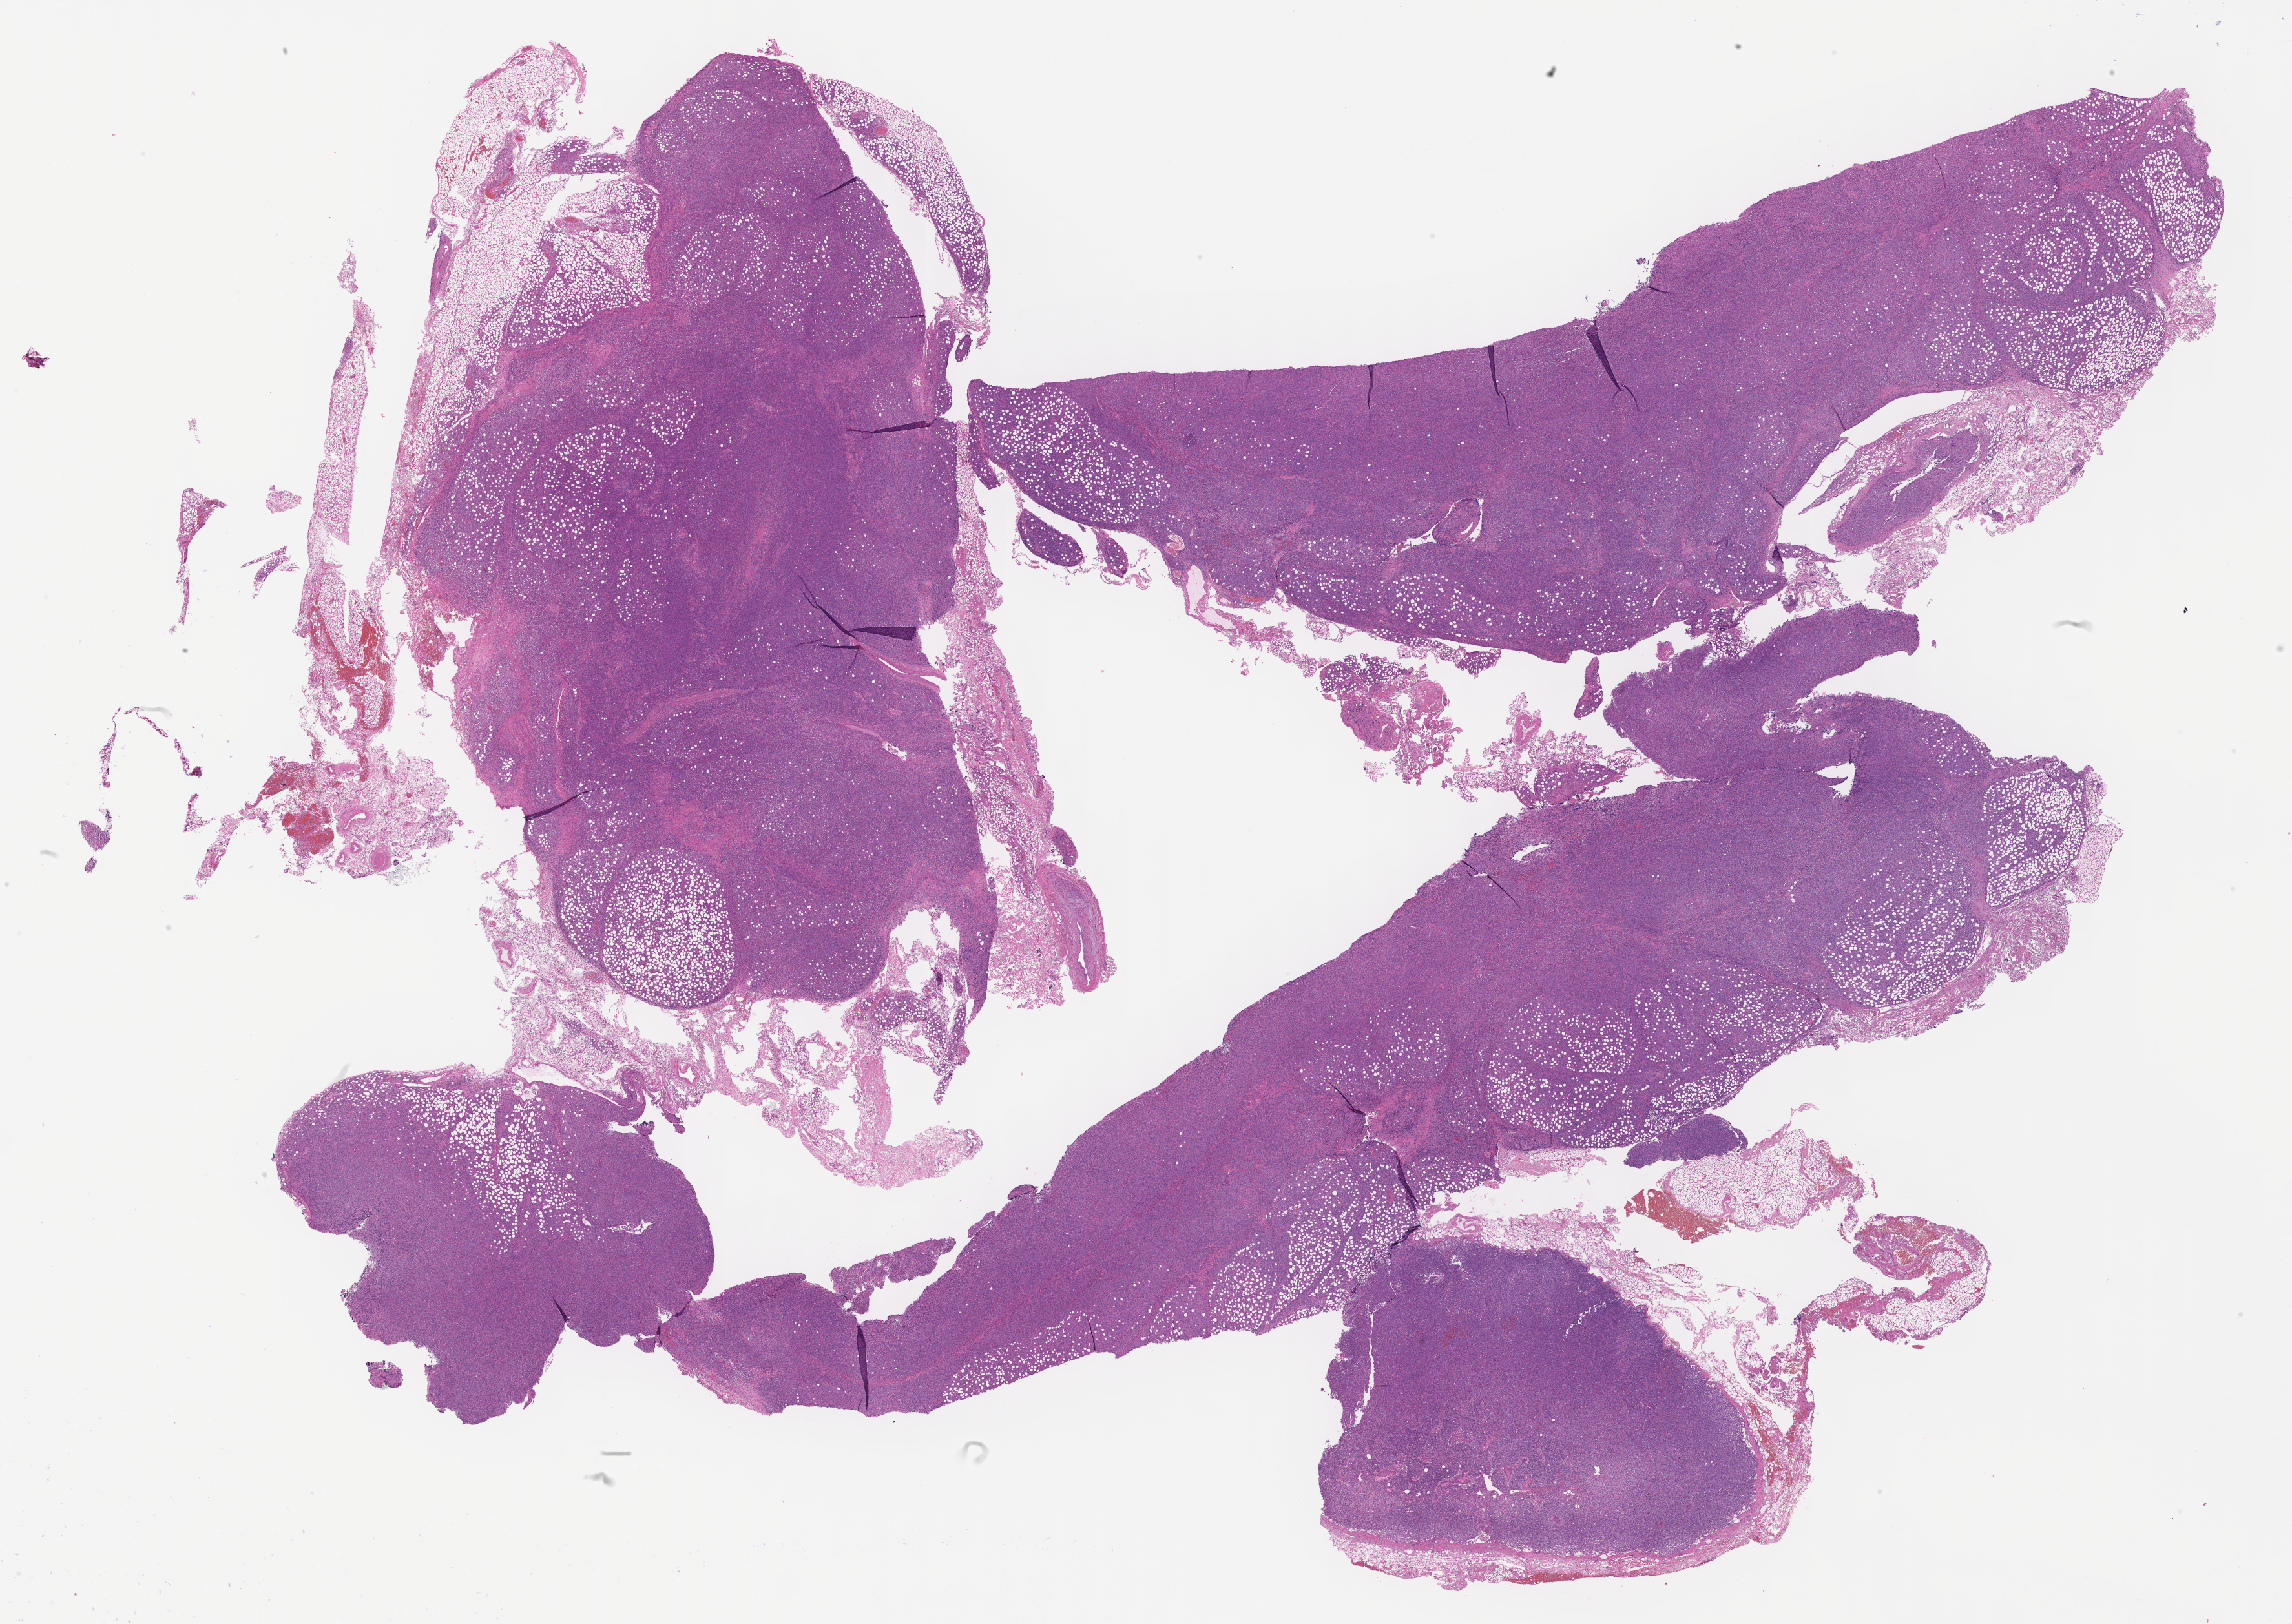
Digitized hematoxylin and eosin (H&E)-stained section, whole scanned area (about 28.7 x 20.3 mm) shown as a low-resolution overview; specimen: tumor tissue; anatomic site: lymph node. Patient male; 68 years old.
Diagnosis: Diffuse large B-cell lymphoma, NOS.